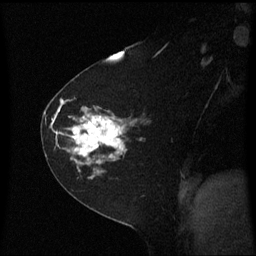
Breast MRI (dynamic contrast-enhanced), one sagittal slice; position 40 of 60 along the scan axis; dynamic contrast-enhanced series, image 2 of 3 at this slice position (ordered by acquisition); 1.5 T; TE 4.2 ms, TR 8.4 ms; 2 mm slice thickness; 256 × 256 image matrix. Patient: female, 60 years. From the clinical record (not read from this slice): setting: breast cancer imaged before/during neoadjuvant chemotherapy; receptor status: triple-negative.
Structures marked on this image (semi-automatic segmentation, software-assisted and operator-edited):
- analysis volume of interest (the breast-tissue region the enhancement analysis was run in; not a lesion): bounding box (x1, y1, x2, y2) in pixels: (45, 99, 149, 182)
- tumour enhancement mask (voxels above the 70 % enhancement threshold inside the analysis volume of interest): (61, 99, 128, 166)